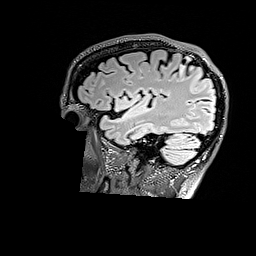
Brain MRI from a brain-tumour surgery series, one sagittal slice; slice 128 of 176 in the series (ordered by position); T2 FLAIR; 256 × 256 image matrix, field of view 256 × 256 mm. From the clinical record (not read from this slice): histopathology: Astrocytoma; WHO grade: 3; IDH mutation: yes; tumour location: Right Parietal.
Annotated regions visible in this slice (manually delineated by an expert):
- tumour: box from (x=178, y=63) to (x=187, y=76) px